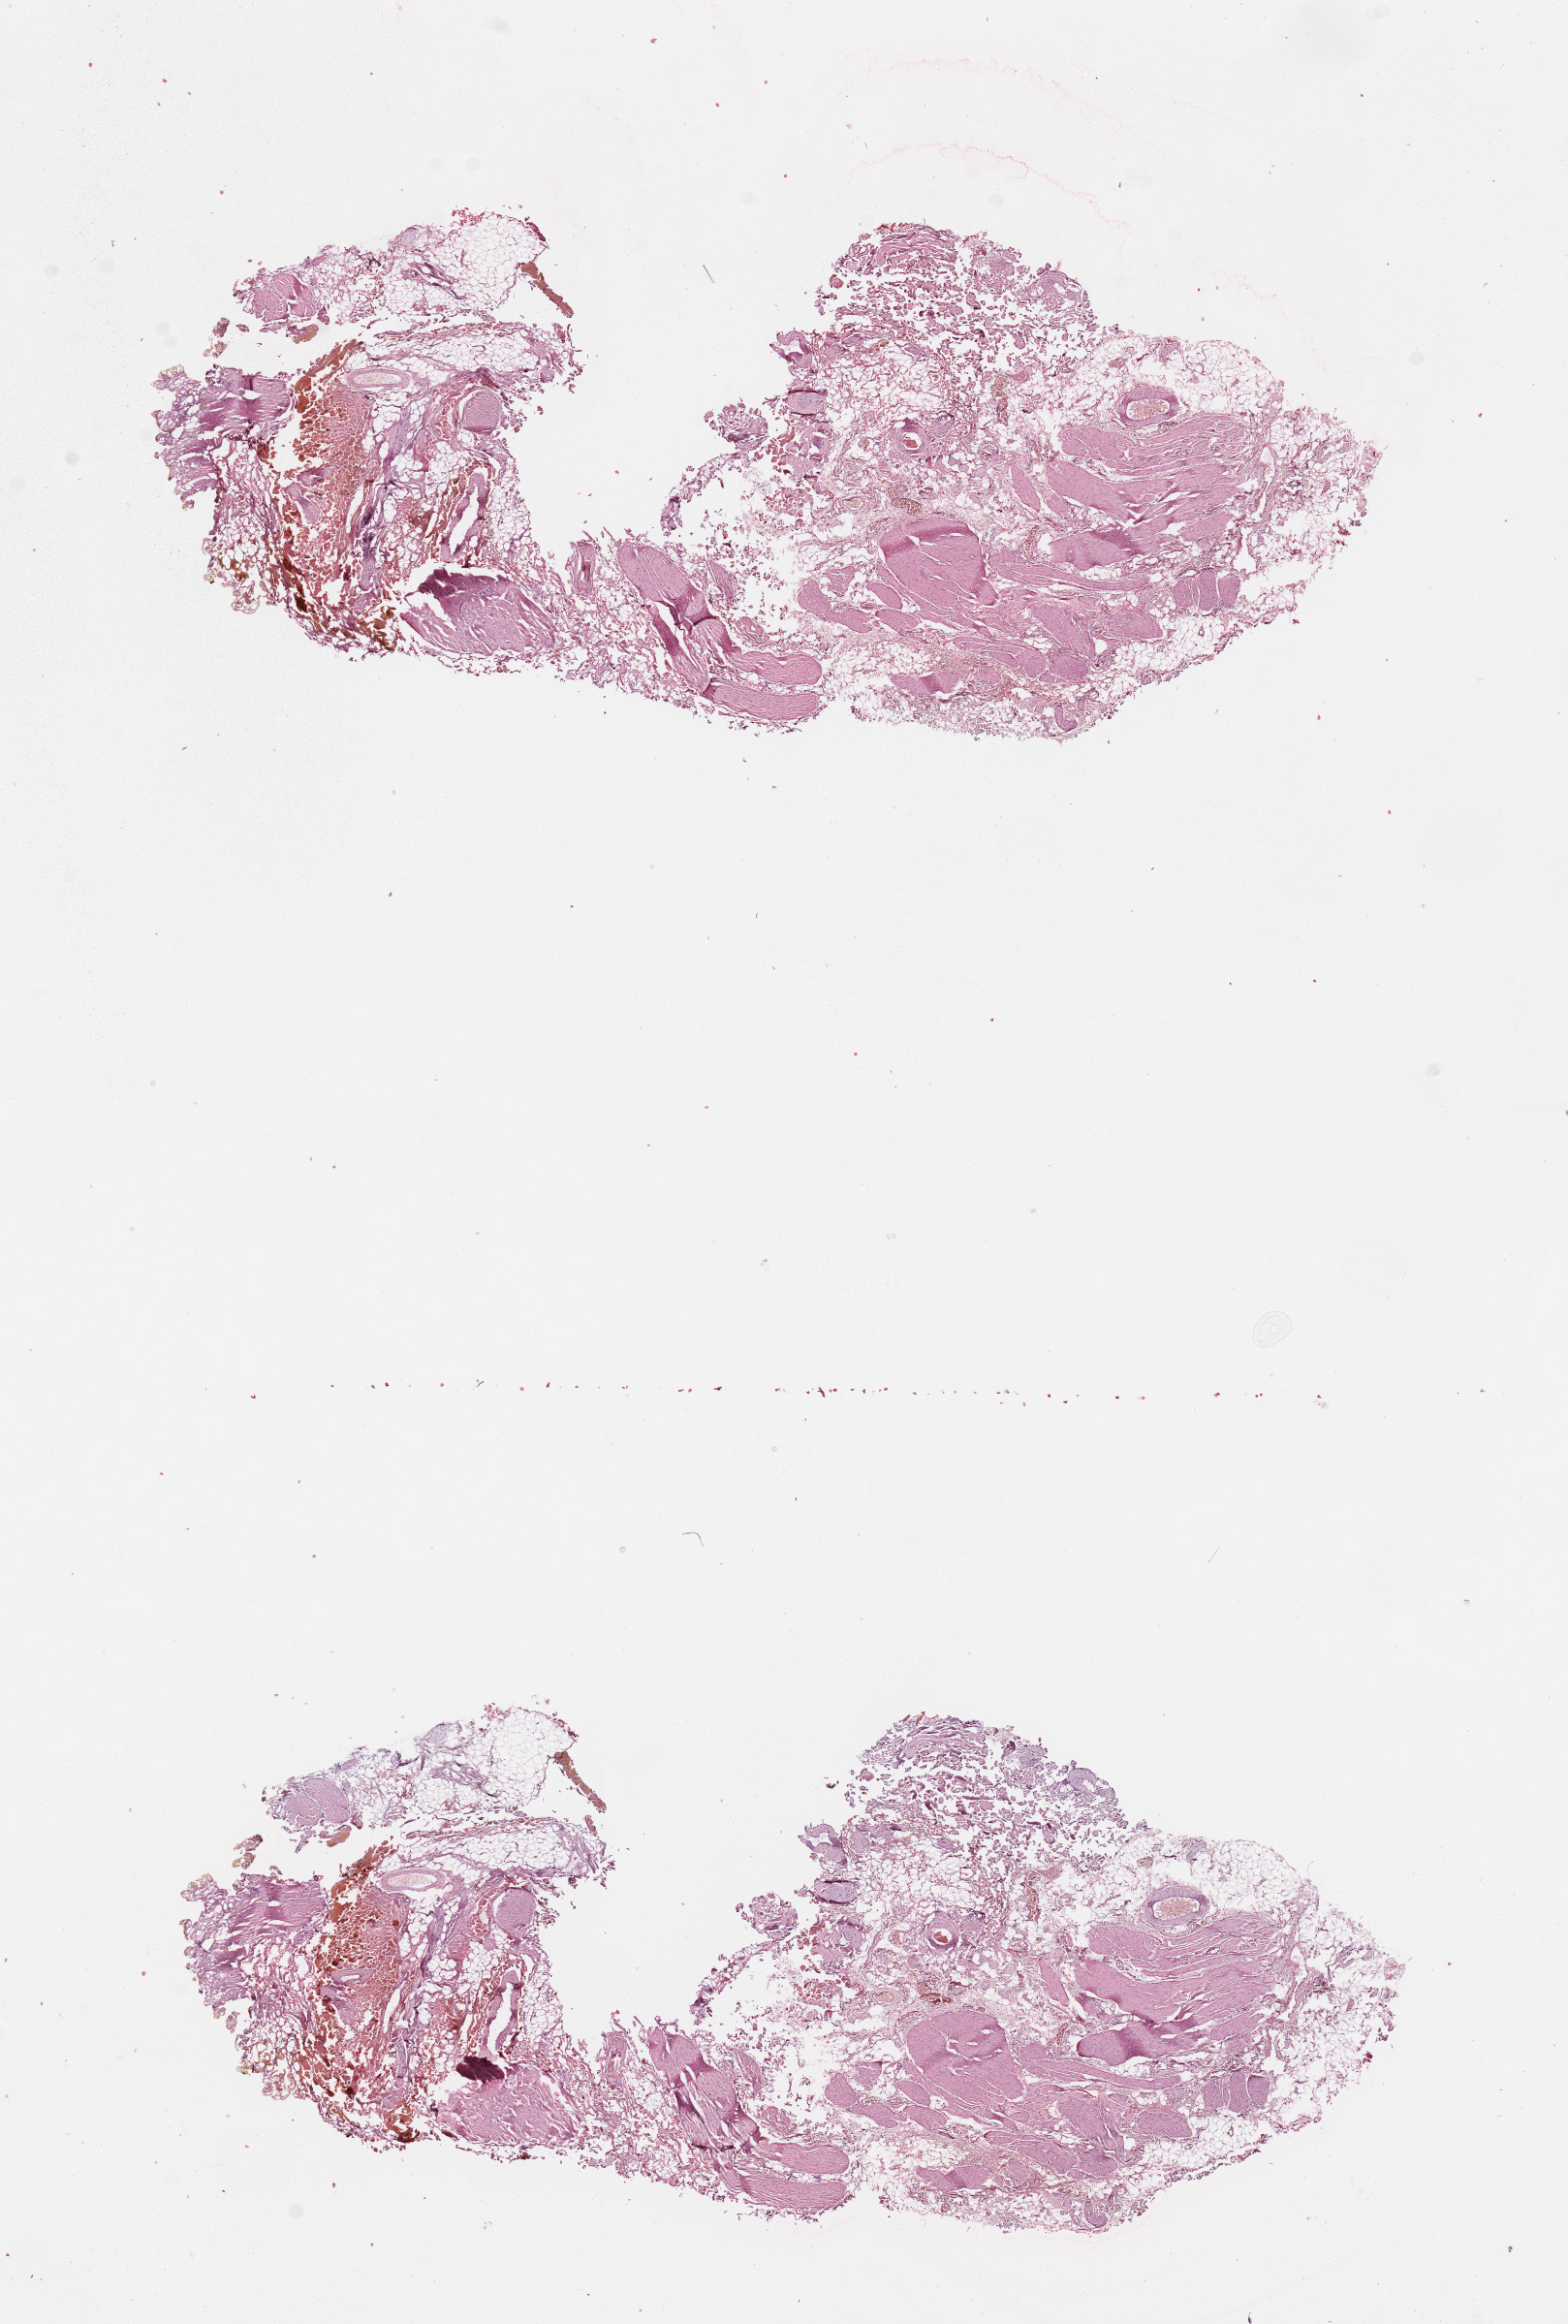
H&E-stained whole-slide image, low-resolution overview of the scanned area, about 12.8 x 19.0 mm (from a 20x scan). 20-year-old male patient.
- patient diagnosis (cohort enrolment): sarcoma (site not recorded at cohort level)